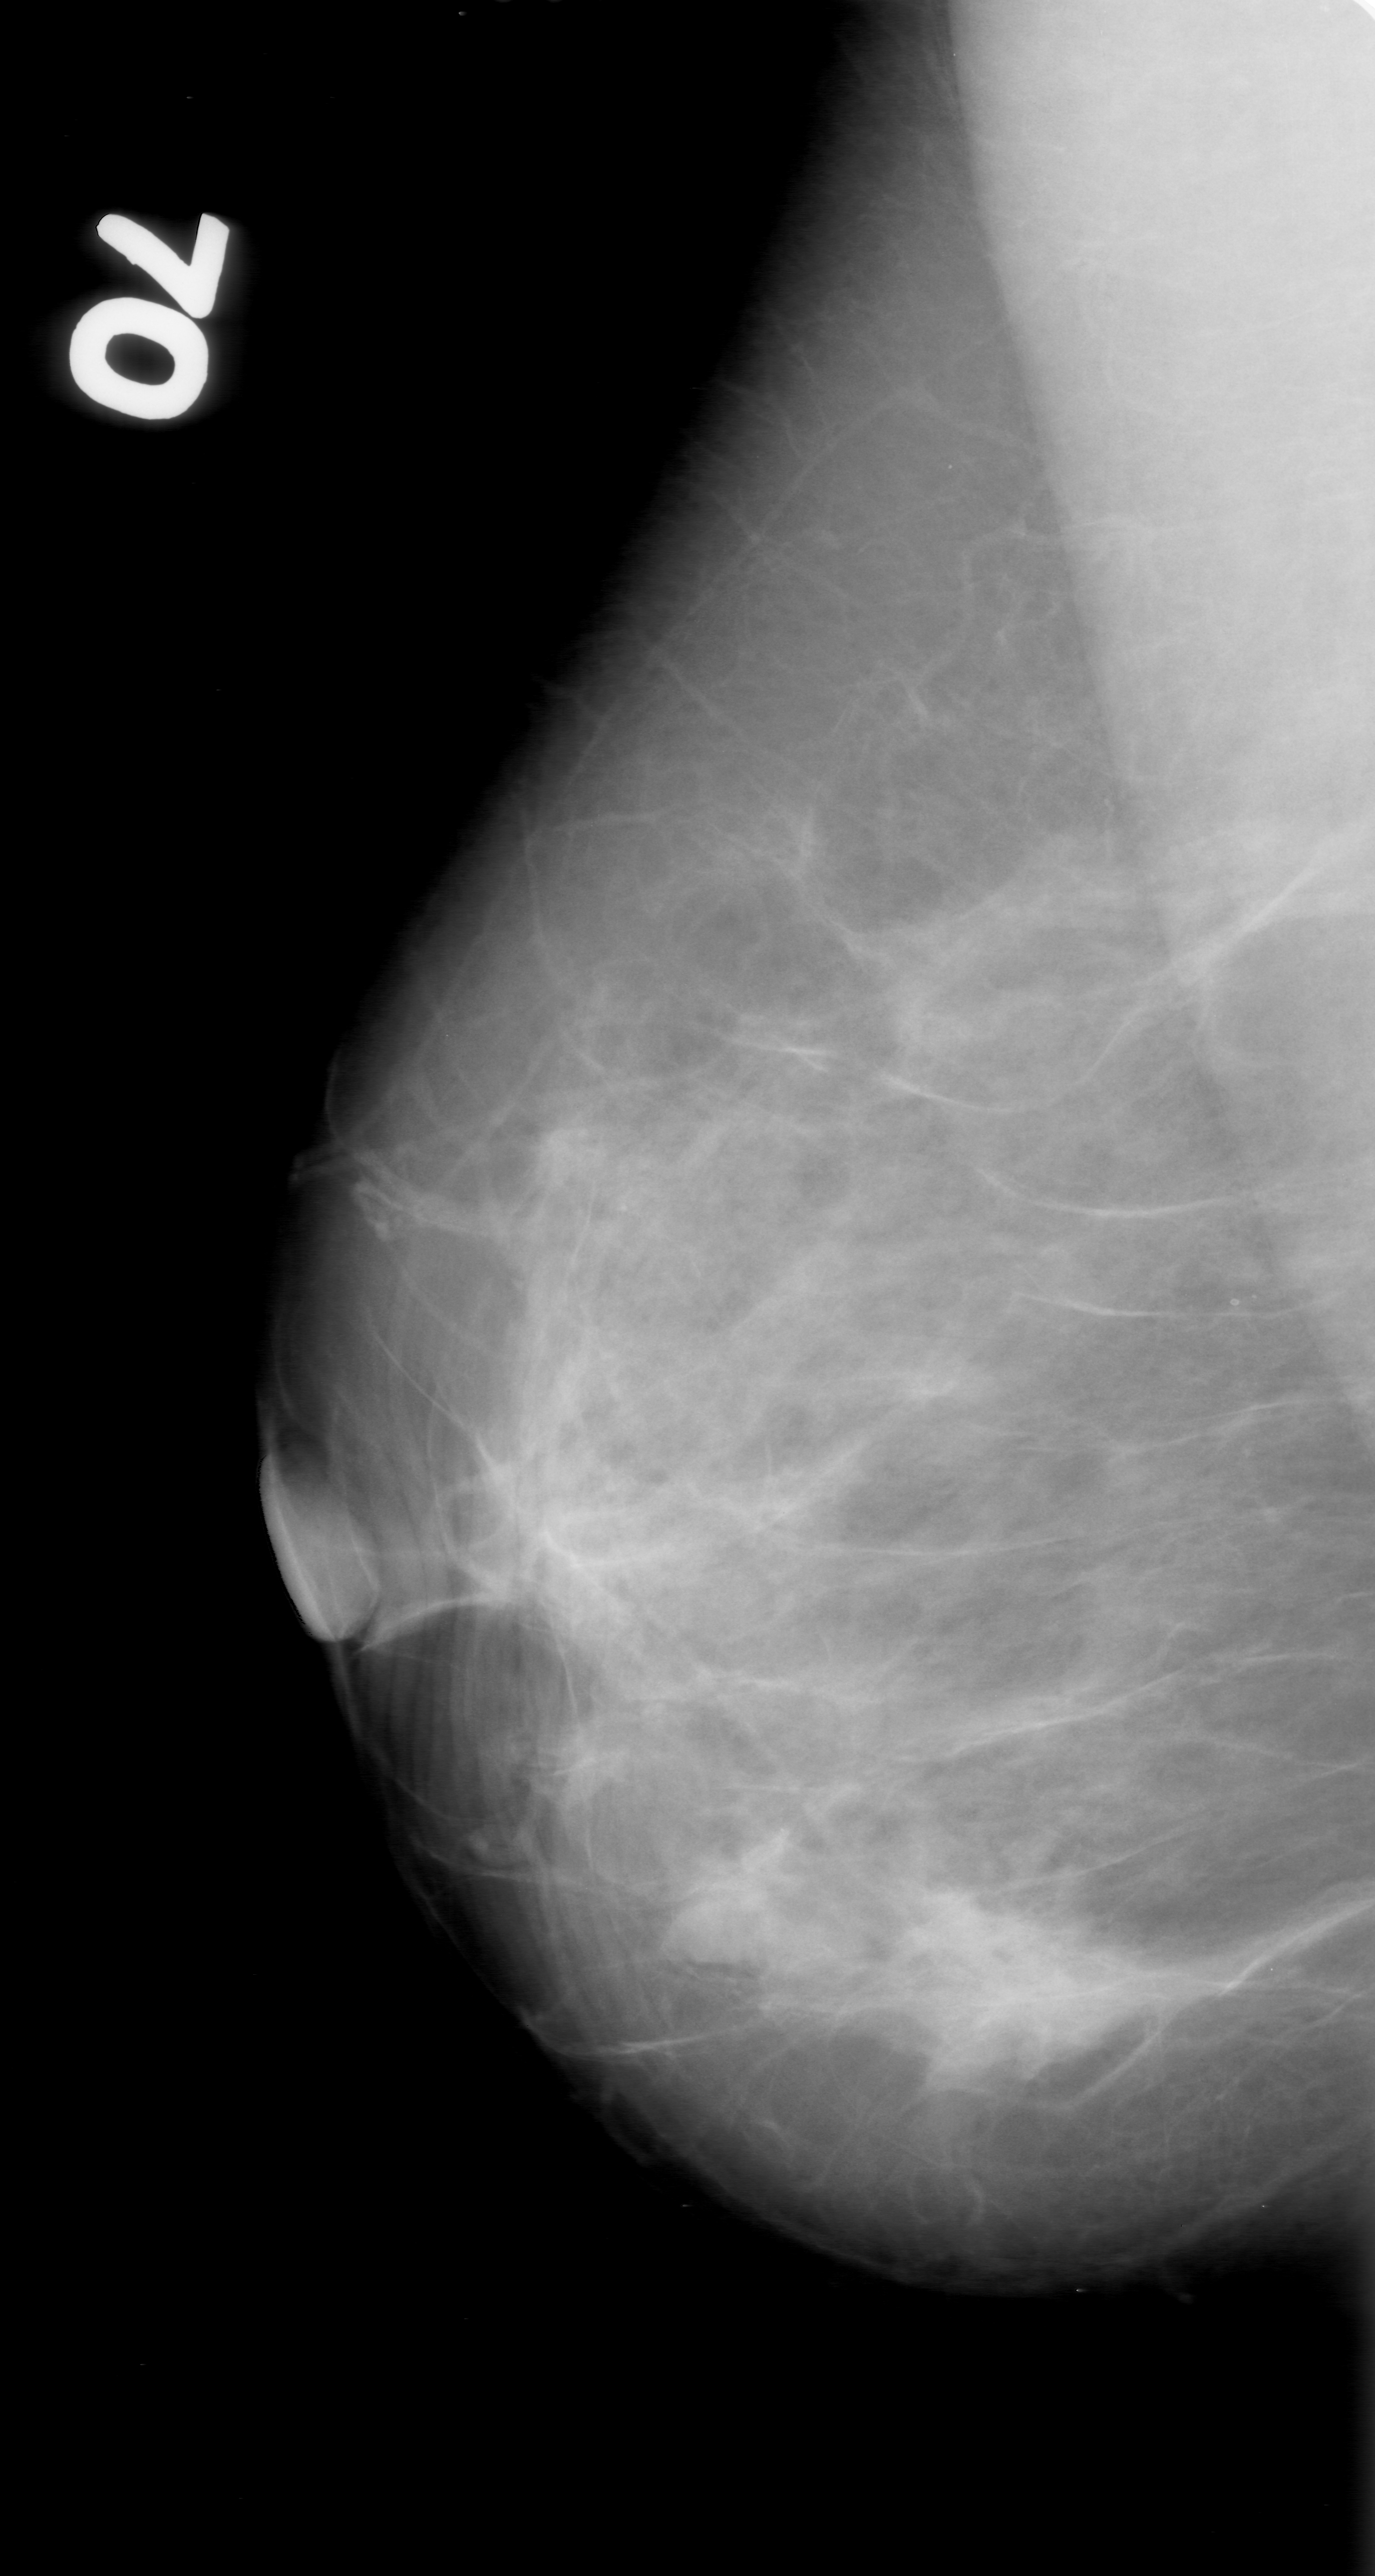
Scanned film-screen mammogram; right breast; MLO view; breast composition: scattered fibroglandular densities (BI-RADS density category 2 of 4).
- Marked abnormality: mass, shape irregular, margins ill defined; BI-RADS assessment category 3; pathology (as recorded): malignant.